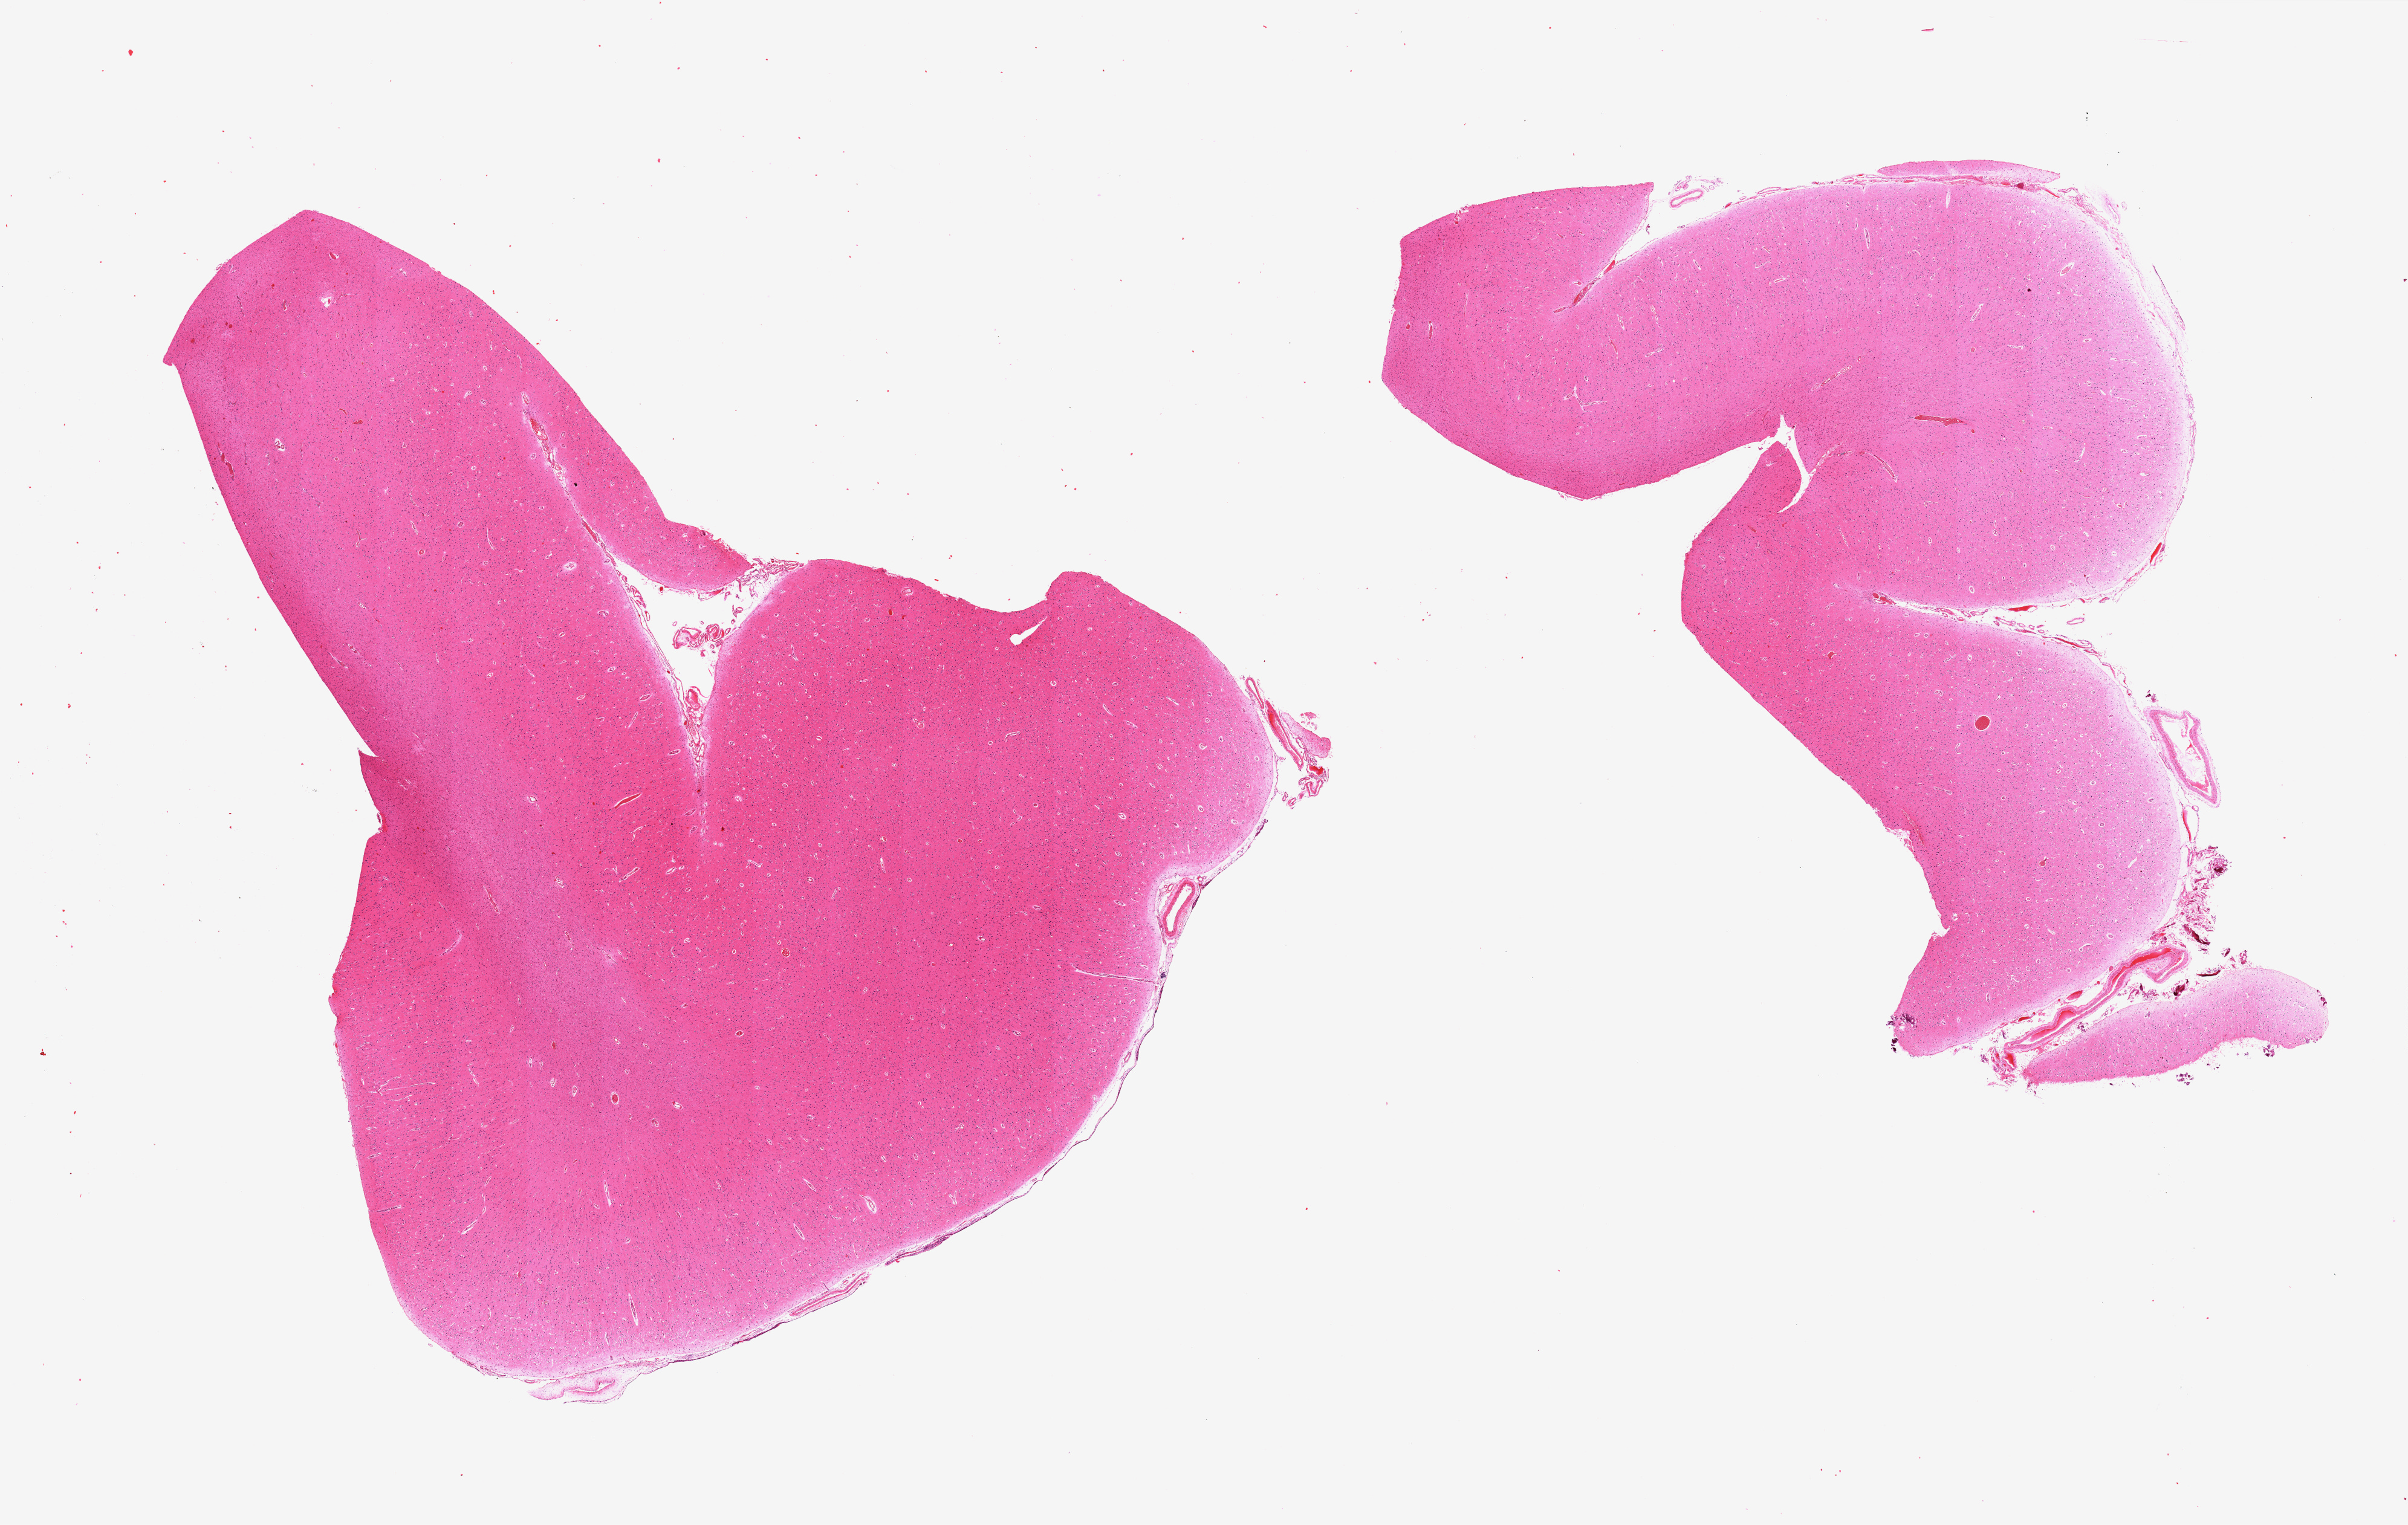
Whole-slide image, H&E stain — shown as a low-resolution overview of the whole scanned area (about 31.5 x 20.0 mm). PAXgene-fixed paraffin-embedded (PFPE) section. Target tissue: cerebral cortex. Donor tissue sample. Male donor.
• review note (as recorded): 2 pieces